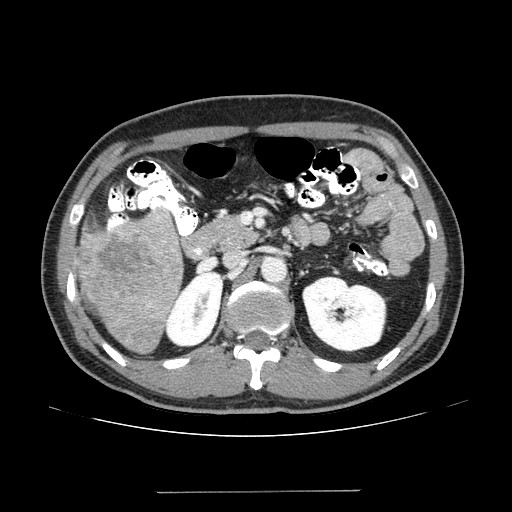
Contrast-enhanced abdominal CT (liver protocol), one axial slice. Slice 66 of 131 in the series (ordered by position). Reconstruction kernel STANDARD. 100 kVp. One of 2 acquisitions stored at this slice position. Soft-tissue window (W 400 / L 40 HU). 512 × 512 image matrix, field of view 380 × 380 mm. From the clinical record (not read from this slice): diagnosis: hepatocellular carcinoma (patient treated with transarterial chemoembolisation; whether this scan precedes or follows treatment is not stated here); TNM stage (as recorded): Stage-I; Child-Pugh class: A; tumour differentiation: poorly differentiated; tumour nodularity: uninodular.
Annotated regions visible in this slice (semi-automatic segmentation, software-assisted and operator-edited):
- liver parenchyma outside the tumour (the mass and vessels are separate outlines, so this box may not span the whole liver): bounding box [x1, y1, x2, y2] px = [74, 210, 182, 354]
- mass: [78, 221, 182, 326]
- liver vessels: [108, 219, 124, 230]